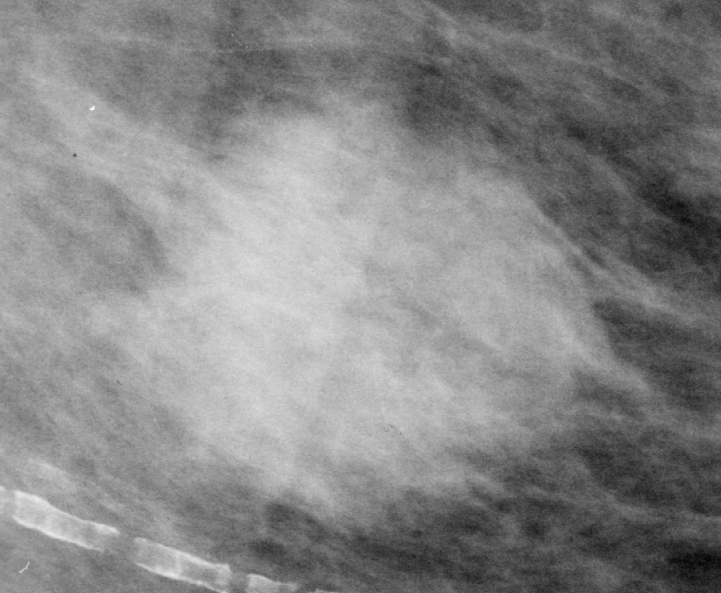
Region of interest cut from a scanned film mammogram (one marked finding), left breast, MLO view.
Finding: calcifications, distribution clustered; BI-RADS assessment category 4; subtlety rating 4 on a 1 (subtle) to 5 (obvious) scale; pathology (as recorded): malignant.